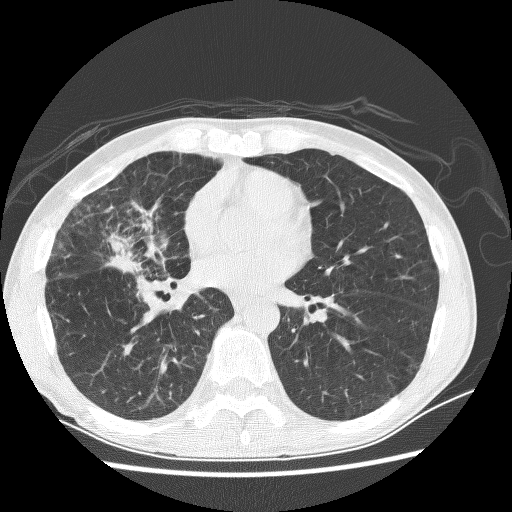
Chest CT (low-dose screening protocol), one axial image; baseline annual screen; lung window (W 1500 / L -600 HU); 2.5 mm slice thickness; lung (sharp) reconstruction kernel (BONE); 512 × 512 image matrix. Male participant, aged 67 years at enrolment. Current smoker at enrolment.
- Expert reader's lesion annotation, bounding box <82,216,175,286> (left, top, right, bottom; pixels).
- Screening reader's record for this exam (one nodule recorded; not confirmed to be the boxed lesion): non-calcified nodule or mass ≥4 mm, right middle lobe, 28 × 18 mm, spiculated (stellate) margins, soft tissue attenuation.
- Official screen result: positive, change unspecified: nodule(s) >= 4 mm or enlarging nodule(s), mass(es), or other non-specific abnormalities suspicious for lung cancer.
- Later outcome: lung cancer diagnosed 69 days after this screen — adenocarcinoma, NOS, right middle lobe, stage IV (AJCC 6th edition), 60 mm at pathology.